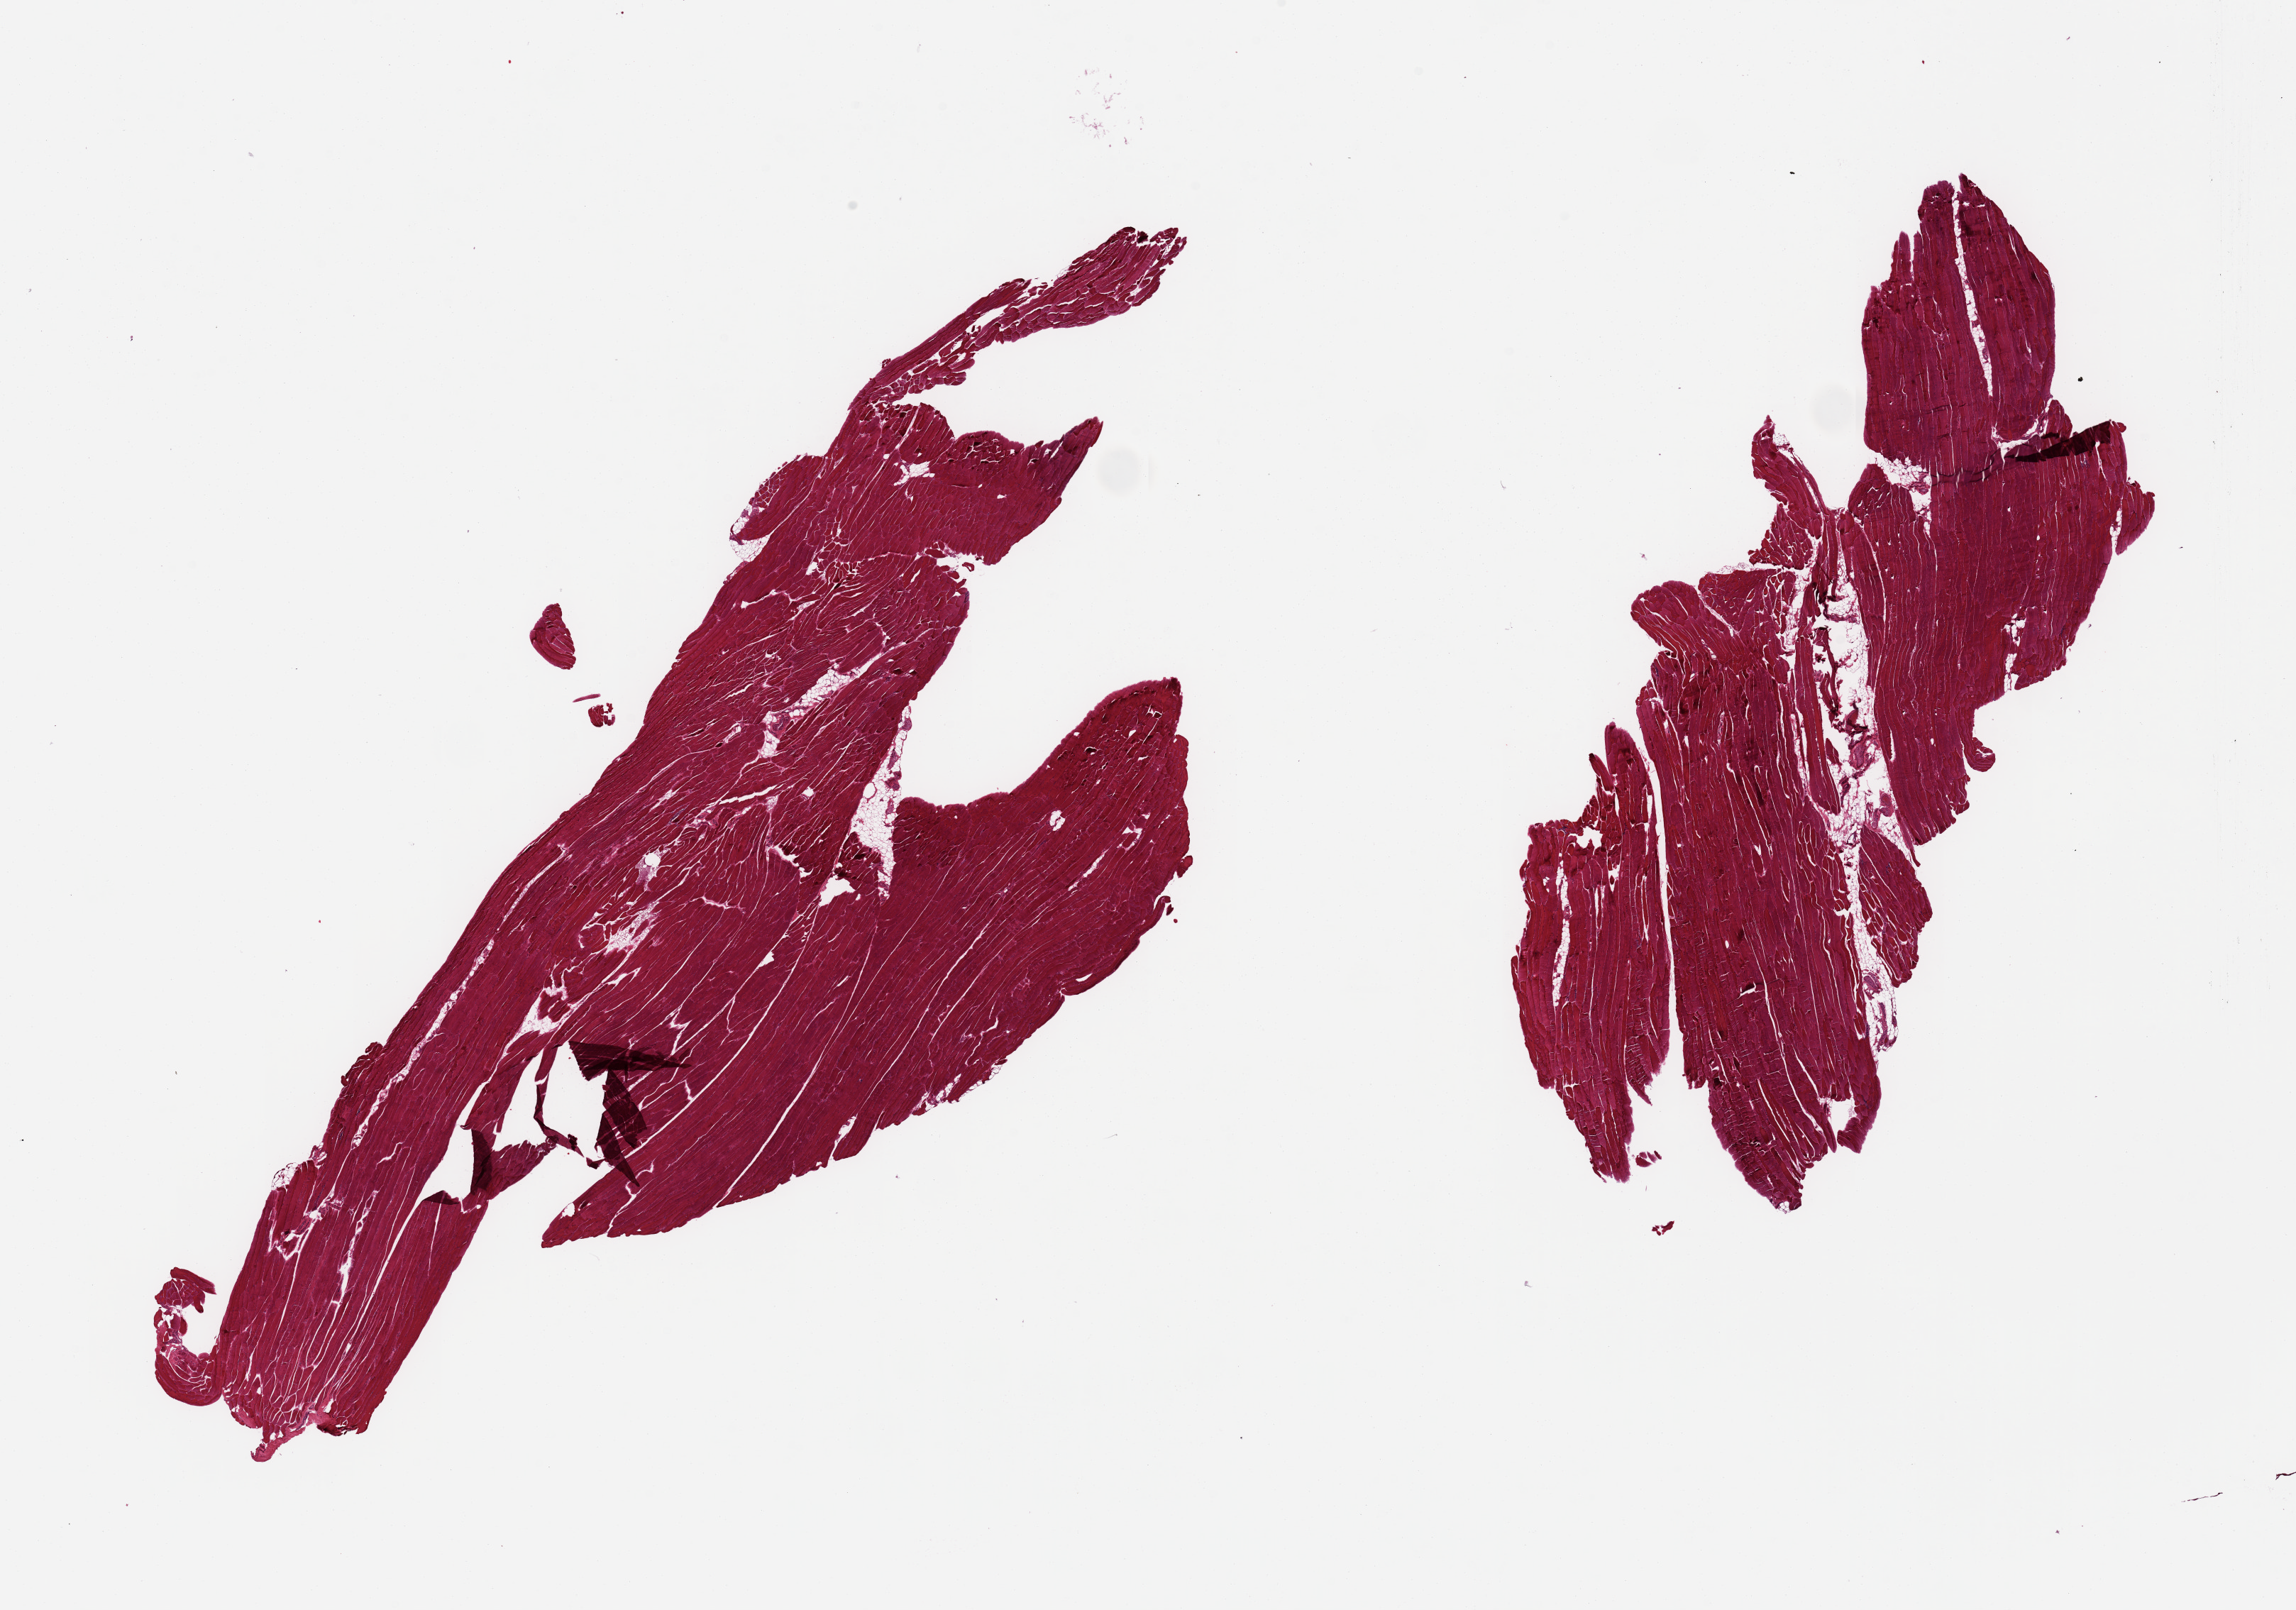
H&E whole-slide image — a low-resolution overview of the entire scanned area, about 25.6 x 17.9 mm (from a 20x scan), PAXgene-fixed, paraffin-embedded tissue, target tissue: skeletal muscle, donor tissue sample. Female donor.
Pathologist's review note for this sample: 2 pieces, interstitial fat/vascular elements are ~10% of tissue.